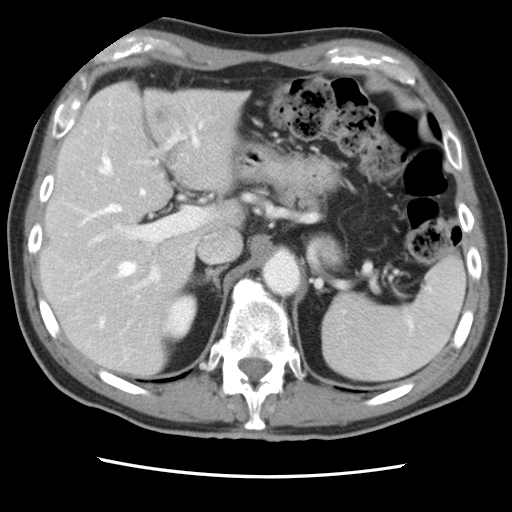
Contrast-enhanced abdominal CT, one axial slice. Position 56 of 83 along the scan axis. 120 kVp. Intravenous contrast given. Soft-tissue window (W 400 / L 40 HU). 5 mm slice thickness. 512 × 512 image matrix, field of view 321 × 321 mm. Male patient, age 69 years. Case-level facts recorded for this patient, not image findings: diagnosis: colorectal cancer liver metastases, imaged before liver resection; multiple liver metastases: yes.
Structures marked on this image (outlined manually by an expert reader):
- hepatic veins: bounding box <83,137,198,327> (left, top, right, bottom; pixels)
- liver: <42,83,245,378>
- planned liver remnant (the part of the liver to remain after resection): <42,140,204,378>
- portal vein (with intrahepatic branches): <88,122,206,290>
- liver metastasis: <156,112,164,118>